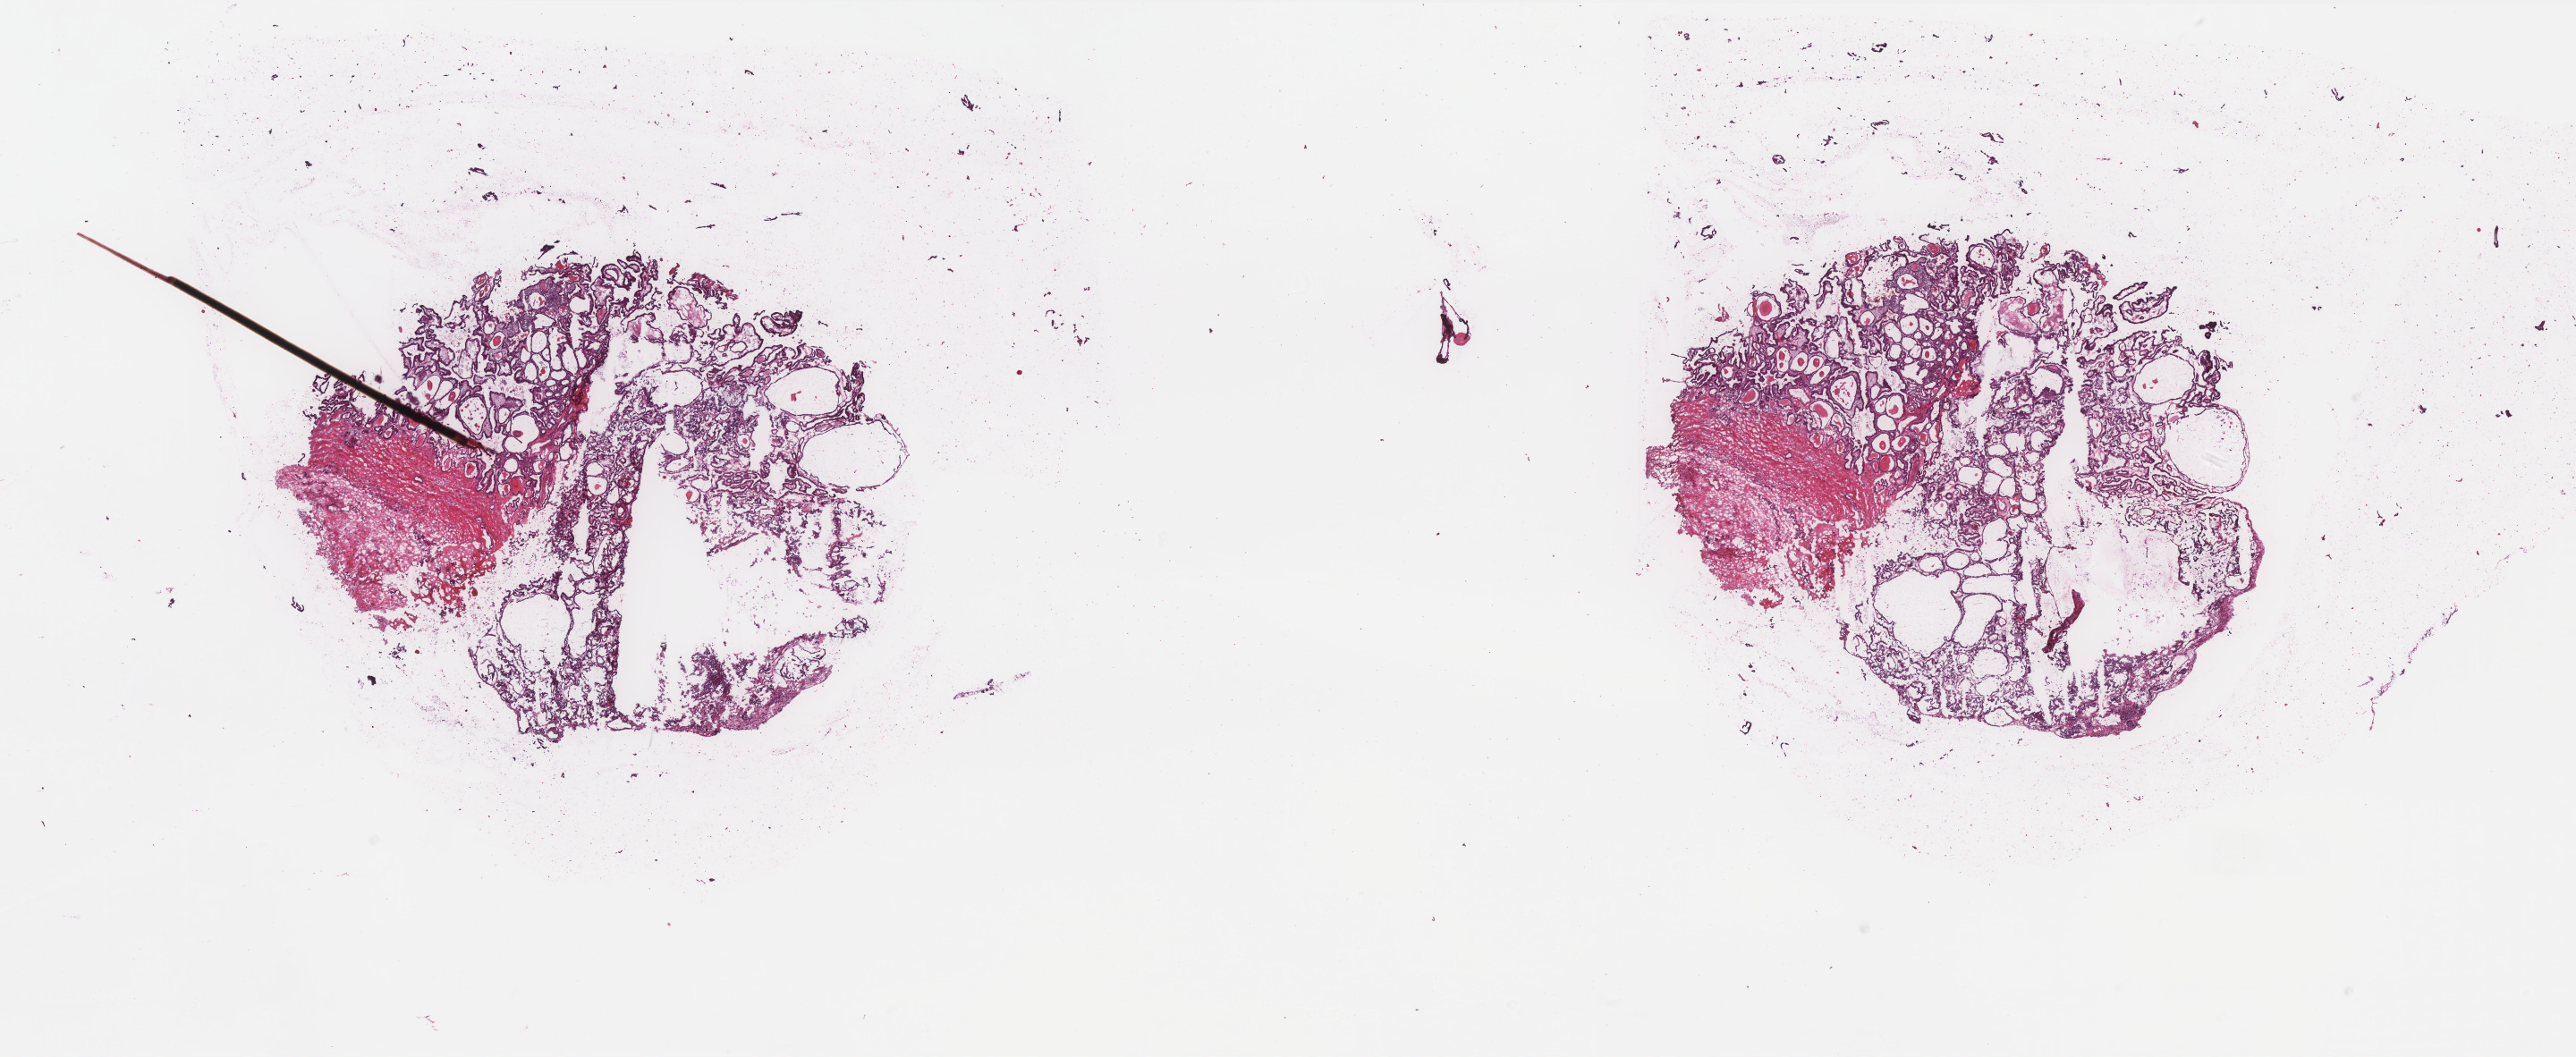
Digitized Hematoxylin and eosin (H&E) stained tissue section (whole slide), shown as a low-resolution overview of the whole scanned area (about 23.1 x 9.5 mm, from a 40x scan), frozen section from the top of the tissue portion, primary tumour sample from the thyroid. Female, age 55 years at initial diagnosis.
Diagnosis: Papillary adenocarcinoma, NOS (thyroid gland).